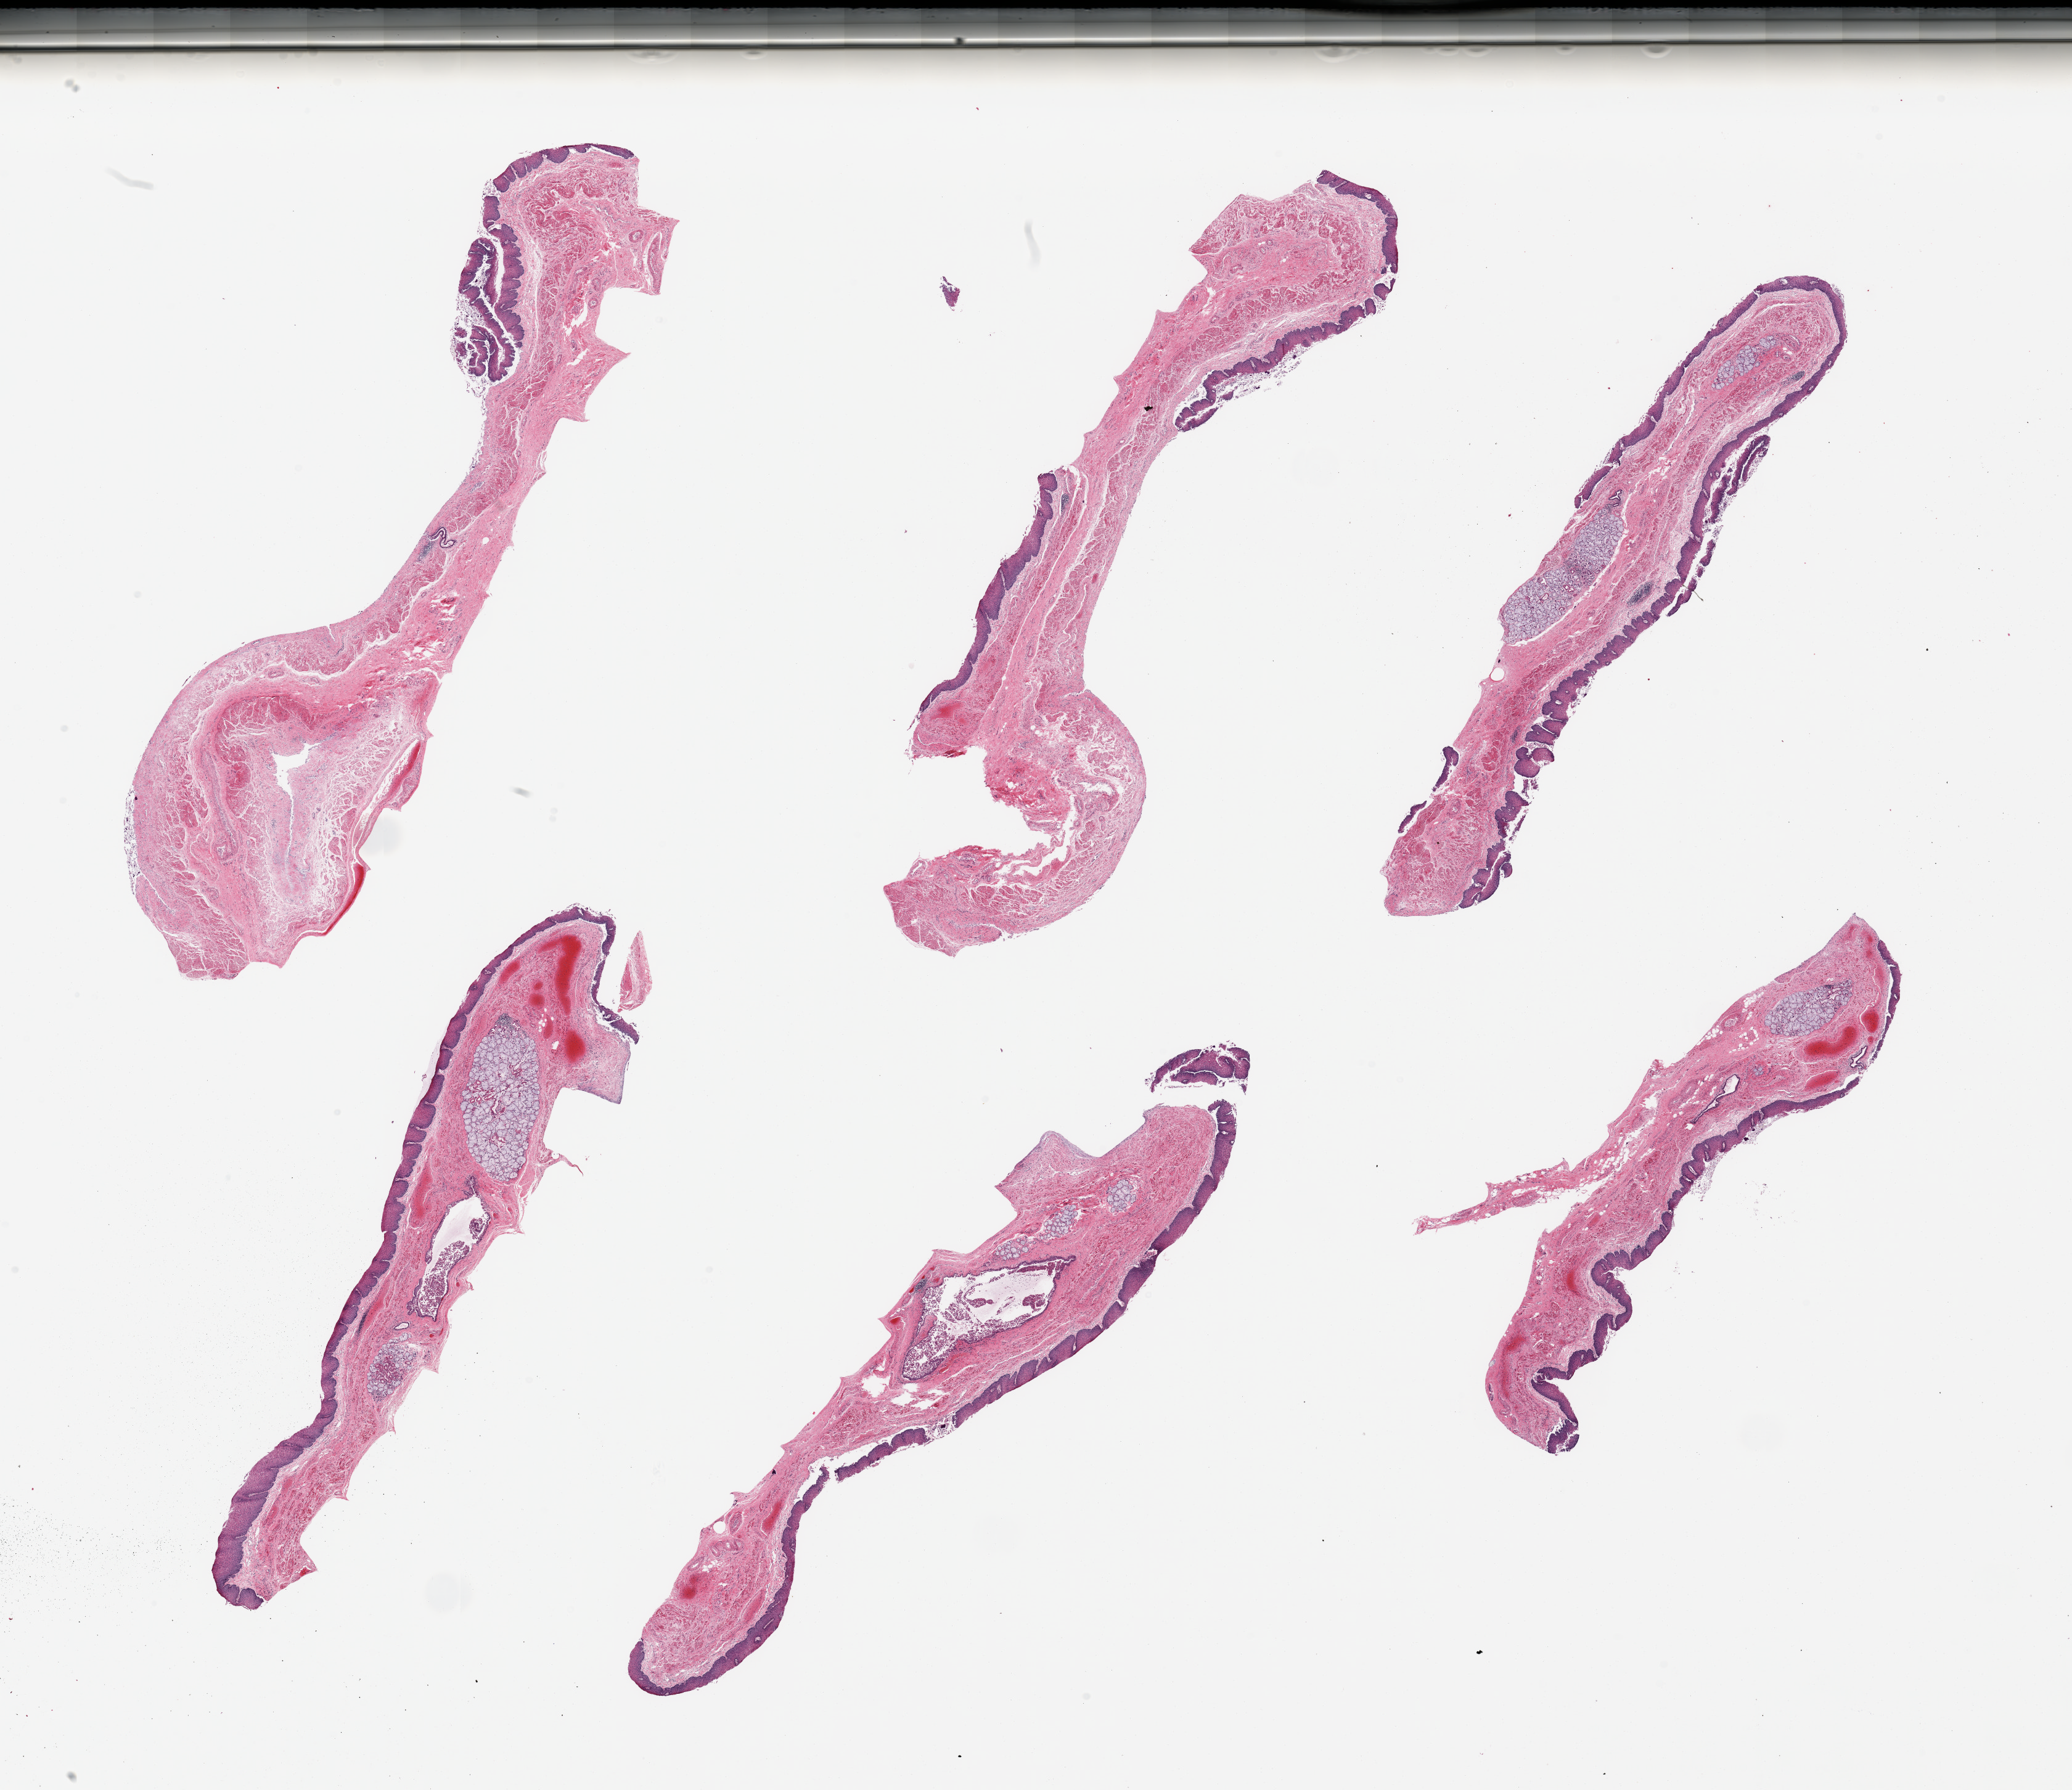
Whole-slide image, H&E stain — whole scanned area (about 26.6 x 23.0 mm) shown as a low-resolution overview; PAXgene-fixed paraffin-embedded (PFPE) section; target tissue: esophageal mucous membrane; tissue donor sample.
Reviewer comment on this tissue sample: 6 pieces; pseudodiverticulosis, several clusters of submucosal glands.